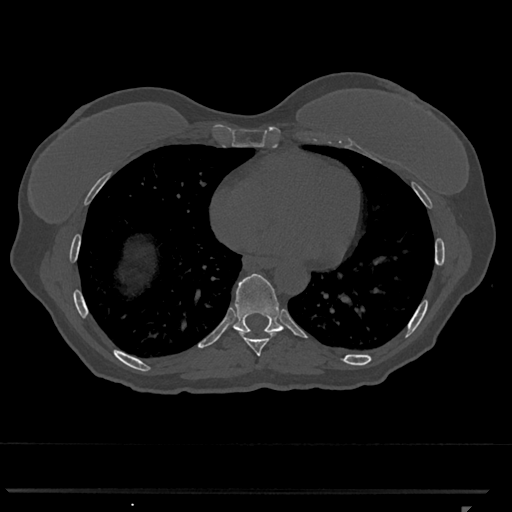
CT including the spine, one axial slice; slice 641 of 793 in the series (ordered by position); reconstruction kernel Br40s/3; 120 kVp; bone window (W 1800 / L 400 HU); 512 × 512 image matrix, field of view 380 × 380 mm. Patient: female, 62 years. From the clinical record (not read from this slice): primary cancer: renal.
Outlined on this slice (semi-automatic segmentation, software-assisted and operator-edited):
- T8 vertebra: box from (x=239, y=332) to (x=275, y=357) px
- T9 vertebra: (x=232, y=274)–(x=284, y=334)